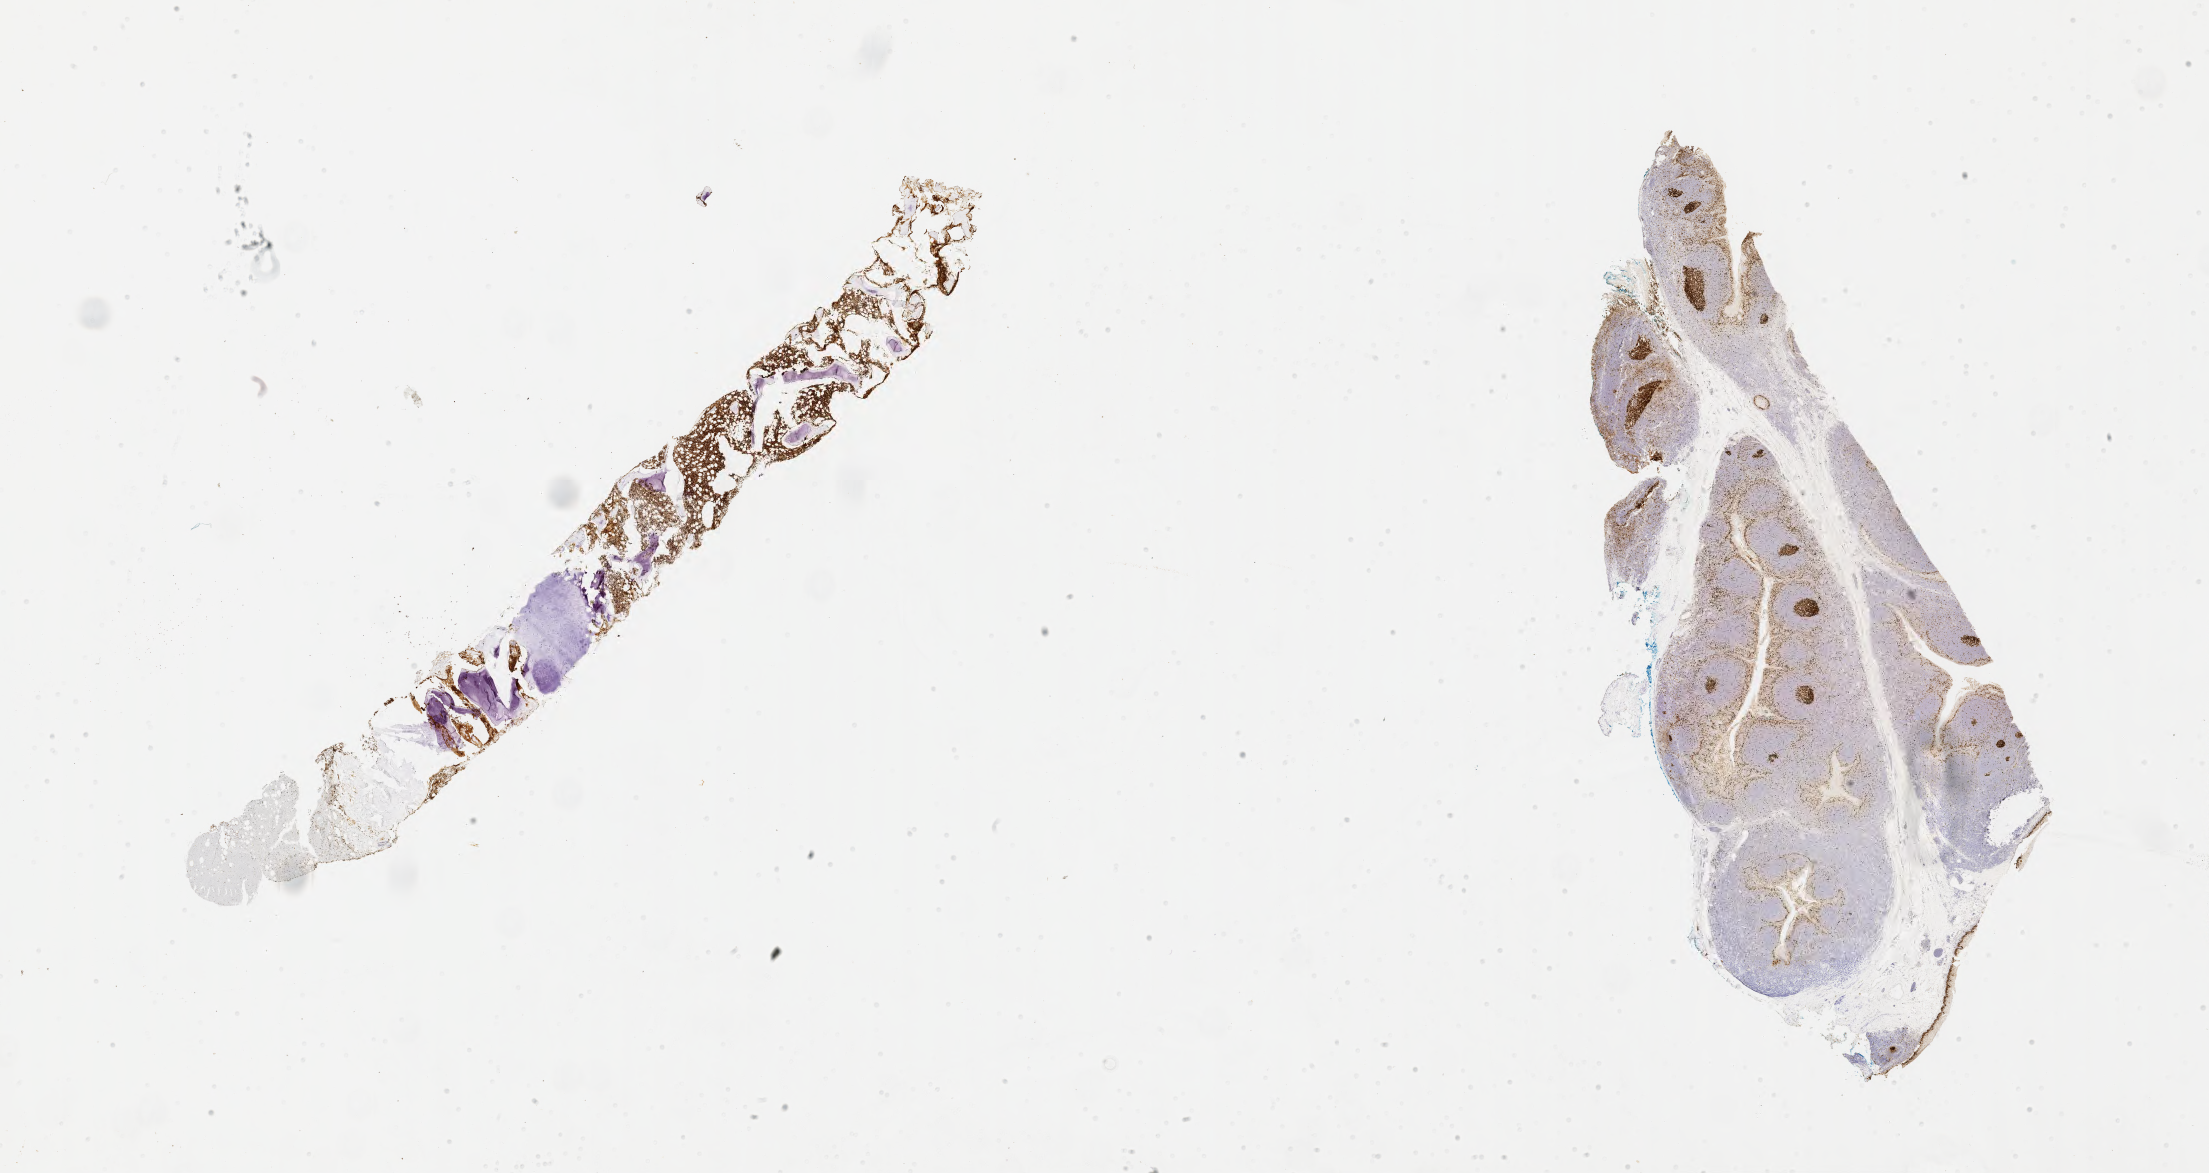
Immunohistochemistry (IHC) whole-slide image stained for Ki-67, shown as a low-resolution overview of the whole scanned area (about 35.7 x 19.0 mm), specimen: tumor tissue, anatomic site: bone marrow. Patient: male, aged 15.
* histologic diagnosis: Burkitt lymphoma, NOS